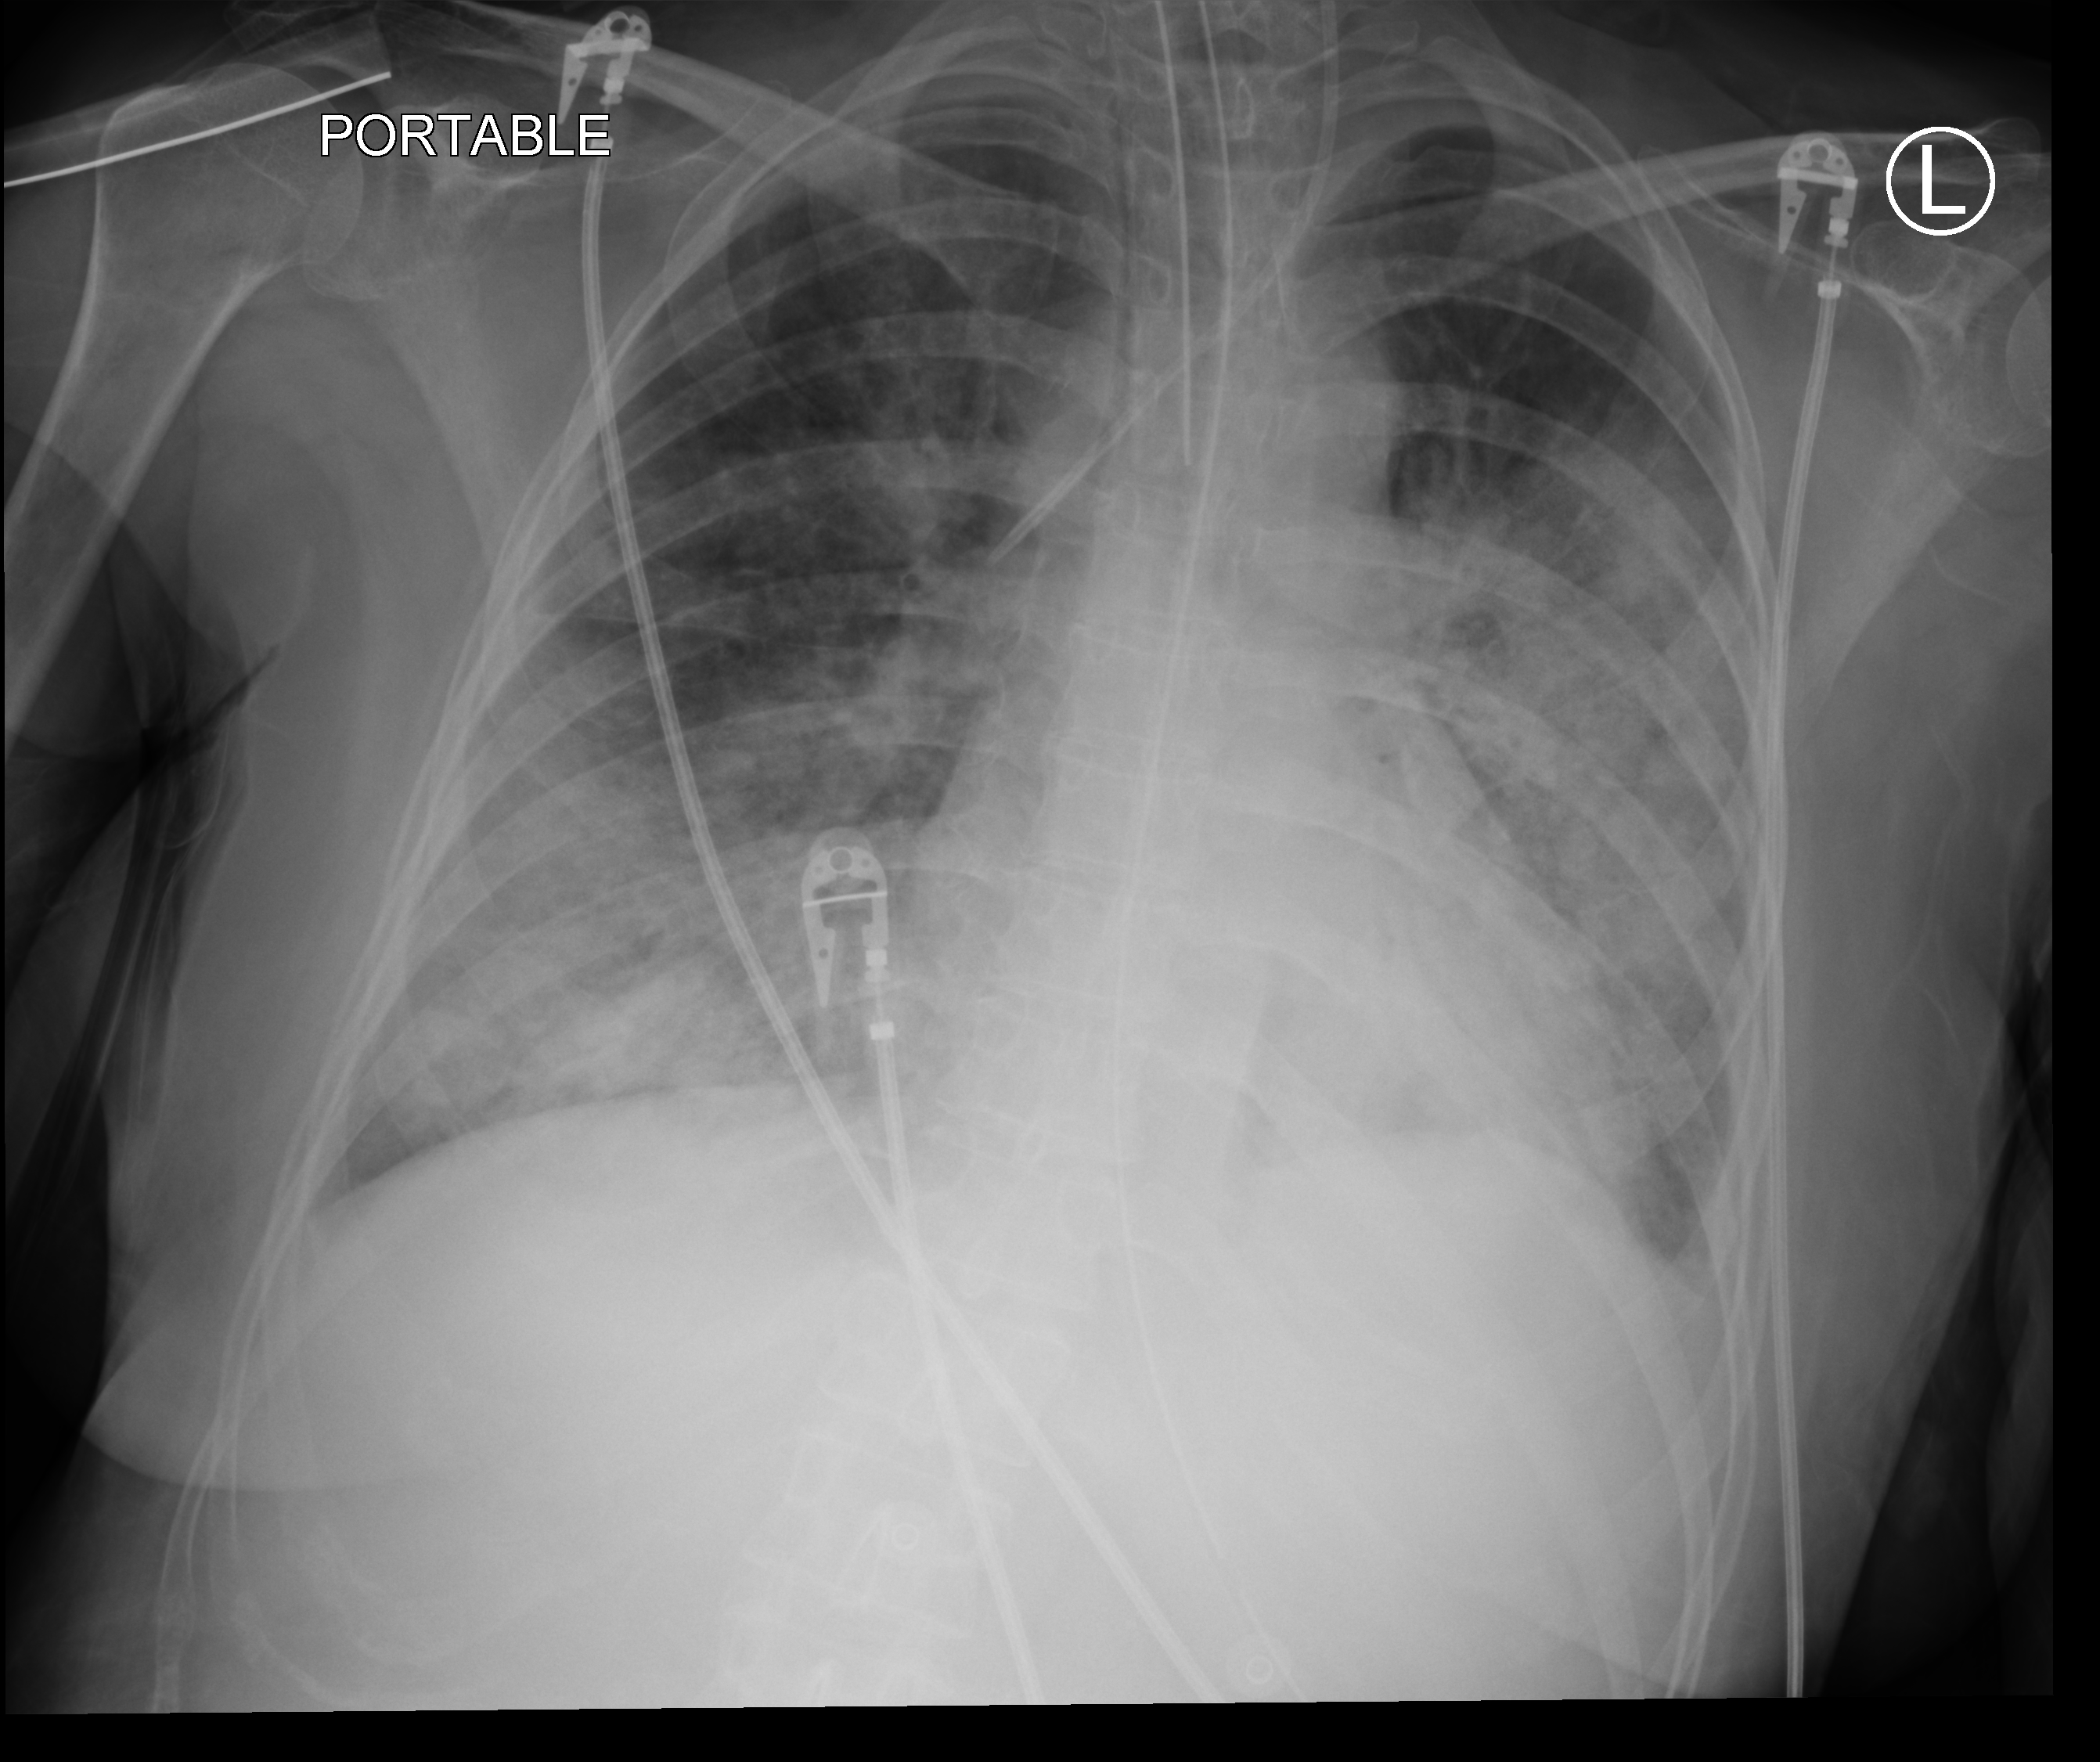
Chest X-ray (portable); anteroposterior (AP) projection. Patient hospitalised with COVID-19, aged 18–59 years.
From the hospital-stay record, not from the radiograph (when in the stay this image was taken is not recorded):
- admitted to intensive care during this hospital stay: yes
- mechanically ventilated during this hospital stay: yes